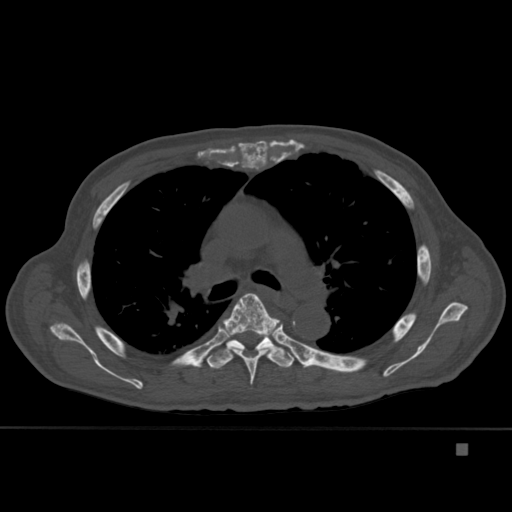
CT including the spine, one axial slice. Position 302 of 451 along the scan axis. Bone window (W 1800 / L 400 HU). 1.5 mm slice thickness. 512 × 512 image matrix, field of view 378 × 378 mm. Male patient, age 75 years. From the clinical record (not read from this slice): primary cancer: prostate.
Annotated regions visible in this slice (semi-automatically segmented with operator editing):
- T5 vertebra: bounding box <218,293,280,385> (left, top, right, bottom; pixels)
- T6 vertebra: <207,331,295,369>